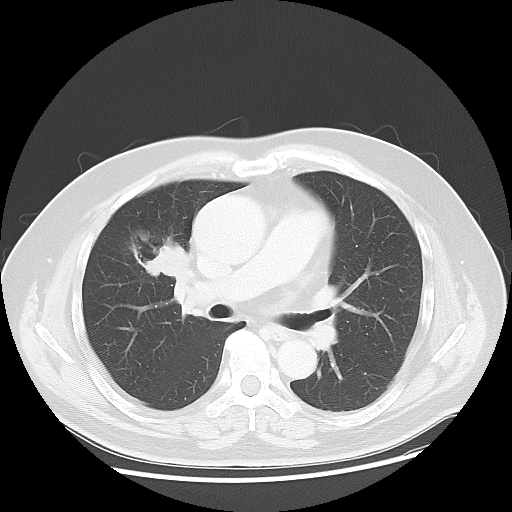
Chest CT, one axial slice. Slice 25 of 48 in the series (ordered by position). Reconstruction kernel LUNG. Lung window (W 1500 / L -600 HU). 5 mm slice thickness. 512 × 512 image matrix, field of view 392 × 392 mm. Patient: male, 60 years. Case-level facts recorded for this patient, not image findings: clinical TNM (as recorded): T2 N3 M0; histopathological grade: G2-3.
Outlined on this slice (rectangle marked by the reading radiologist):
- lung tumour (recorded histology: adenocarcinoma): bounding box (x1, y1, x2, y2) in pixels: (126, 226, 190, 291)